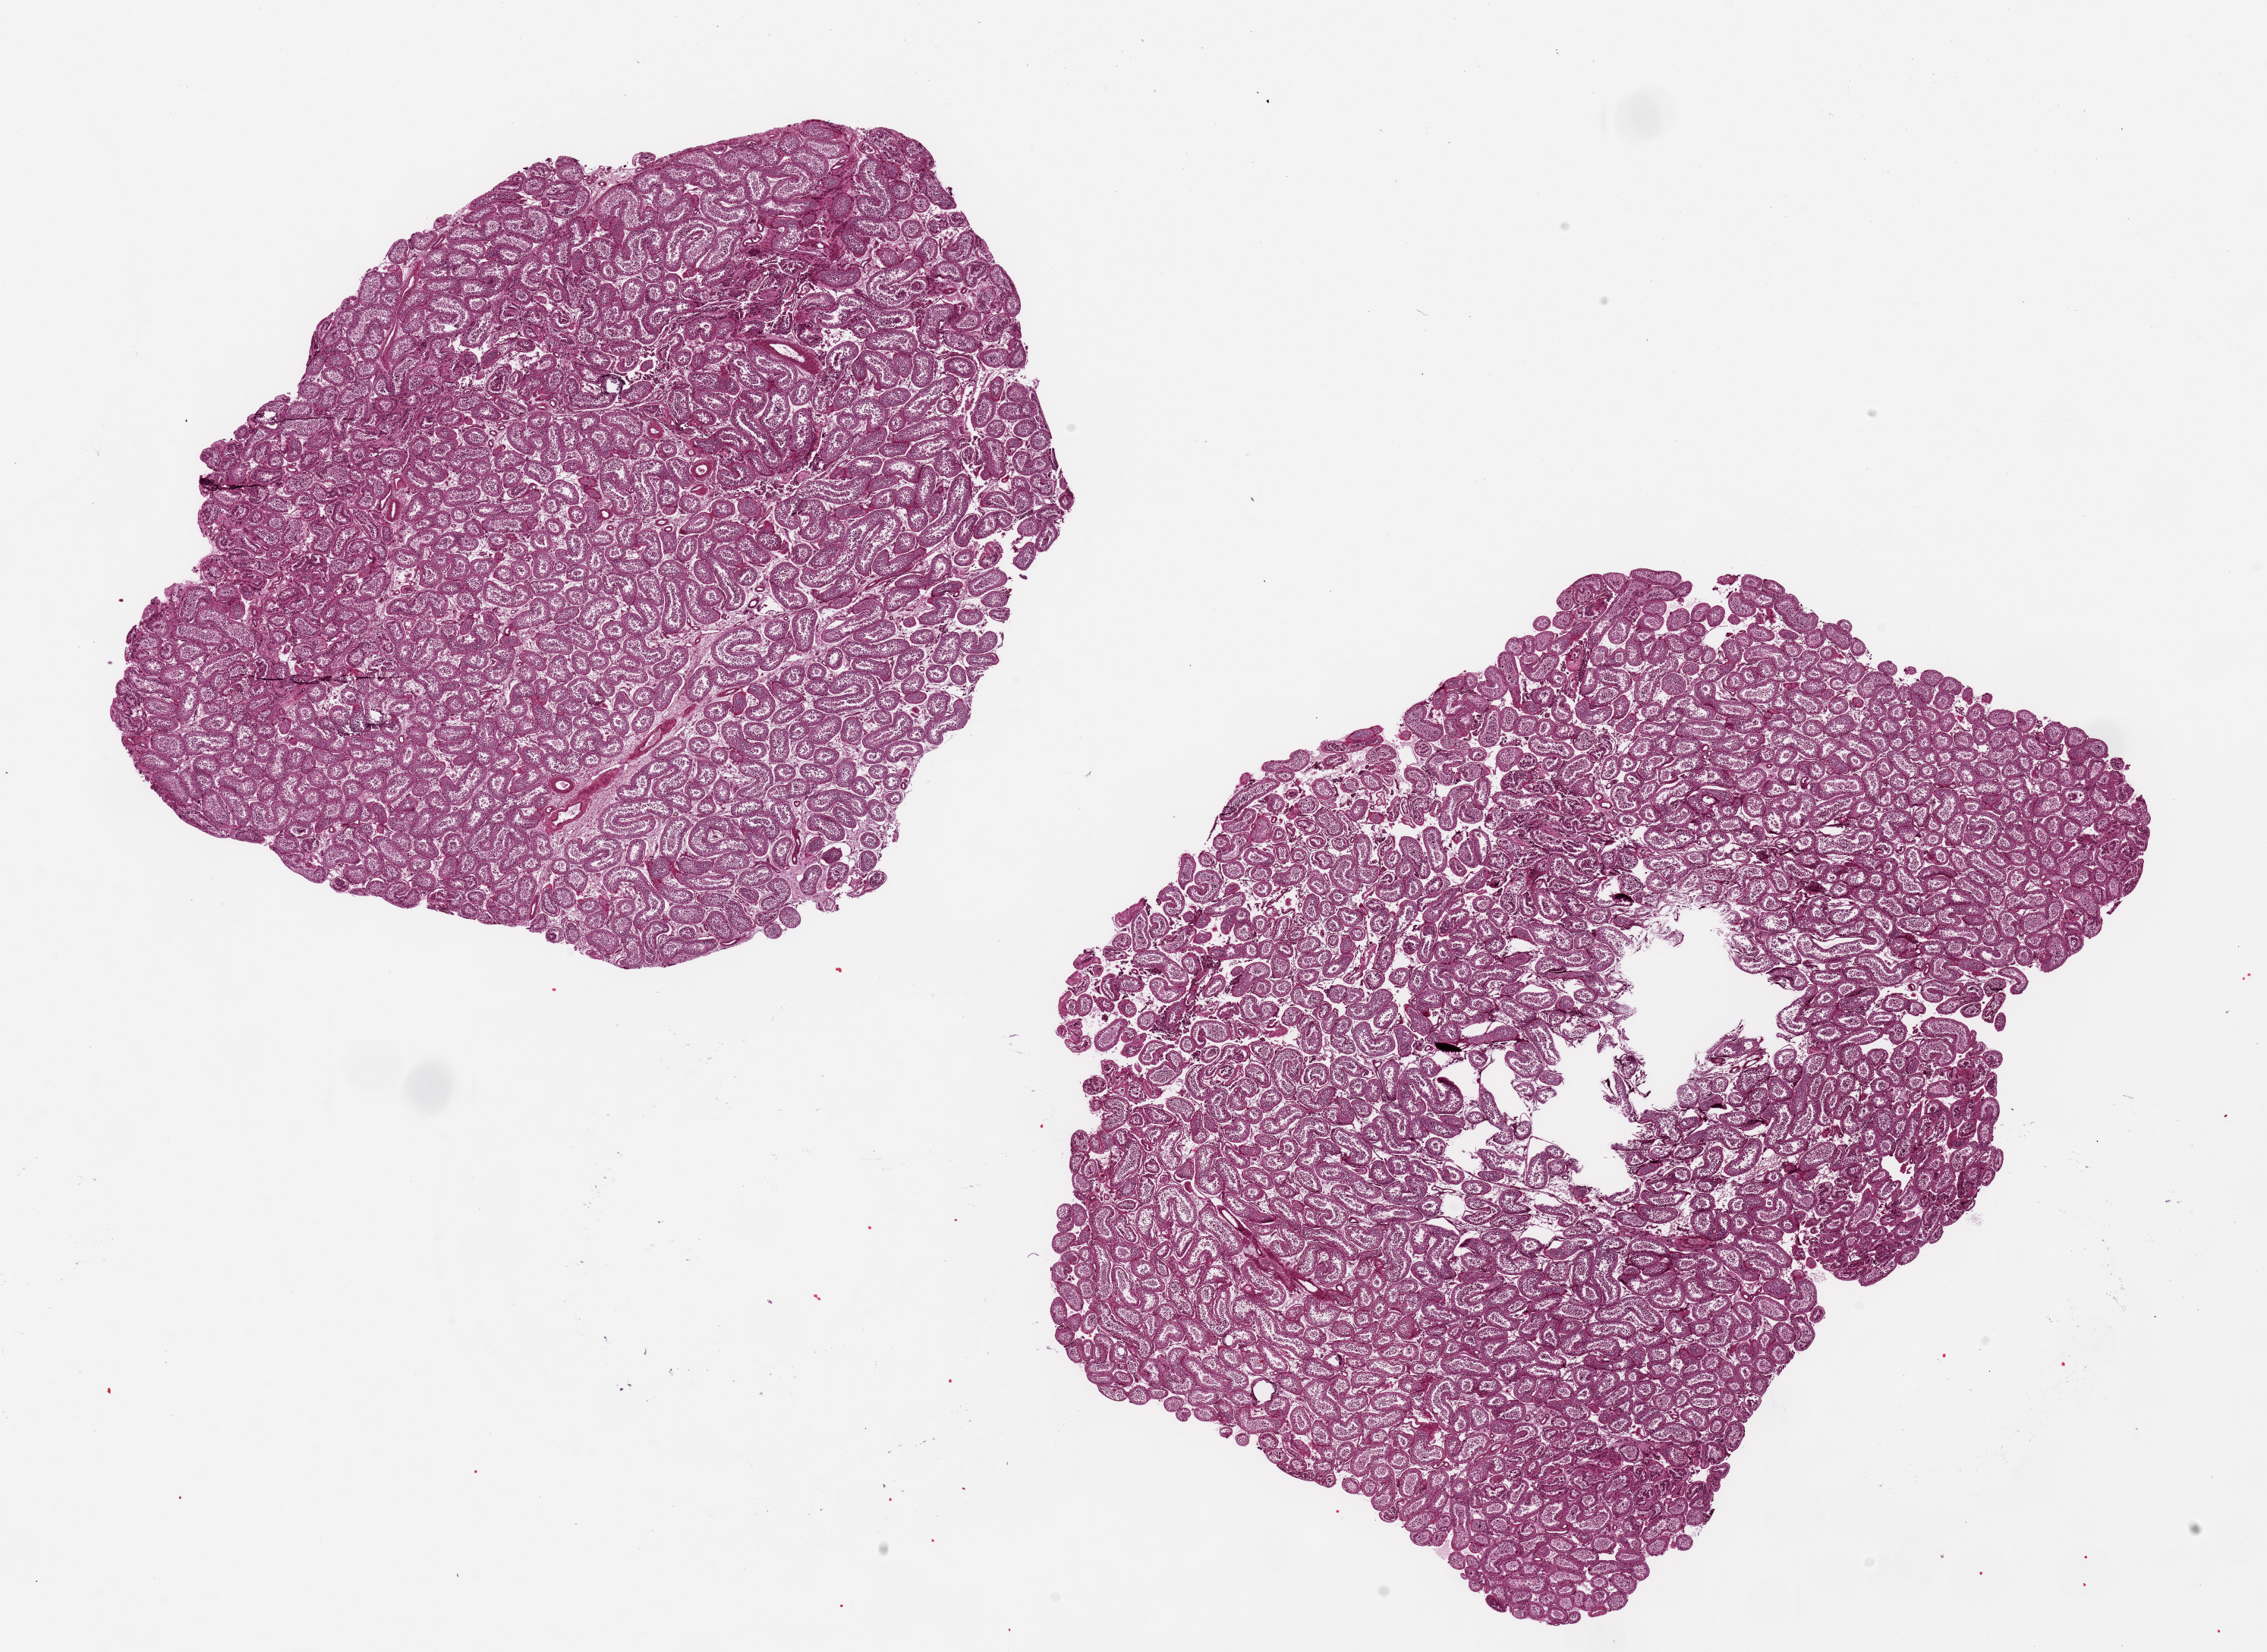
Whole-slide image, hematoxylin and eosin (H&E) stain, brightfield — a low-resolution overview of the entire scanned area, about 23.6 x 17.2 mm (from a 20x scan); PAXgene-fixed, paraffin-embedded tissue; section of testis (target tissue); donor tissue sample.
* review note (as recorded): 2 ~10x8mm aliquots, one with area of central under-fixation